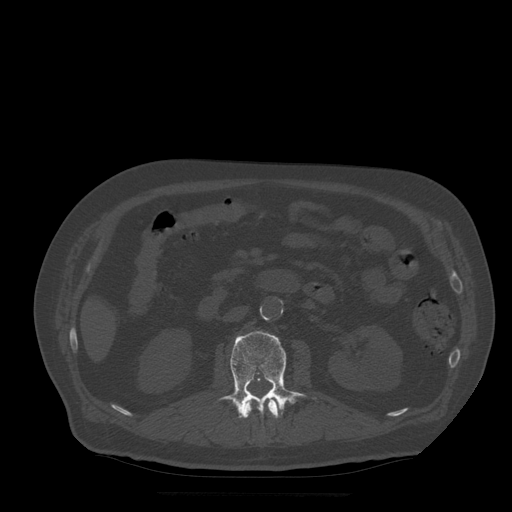
CT including the spine, one axial slice; position 171 of 522 along the scan axis; bone window (W 1800 / L 400 HU); 1.25 mm slice thickness; 512 × 512 image matrix. Patient age 72 years. From the clinical record (not read from this slice): primary cancer: prostate.
Annotated regions visible in this slice (semi-automatically segmented with operator editing):
- L1 vertebra: box from (x=243, y=398) to (x=282, y=419) px
- L2 vertebra: (x=219, y=331)–(x=308, y=419)